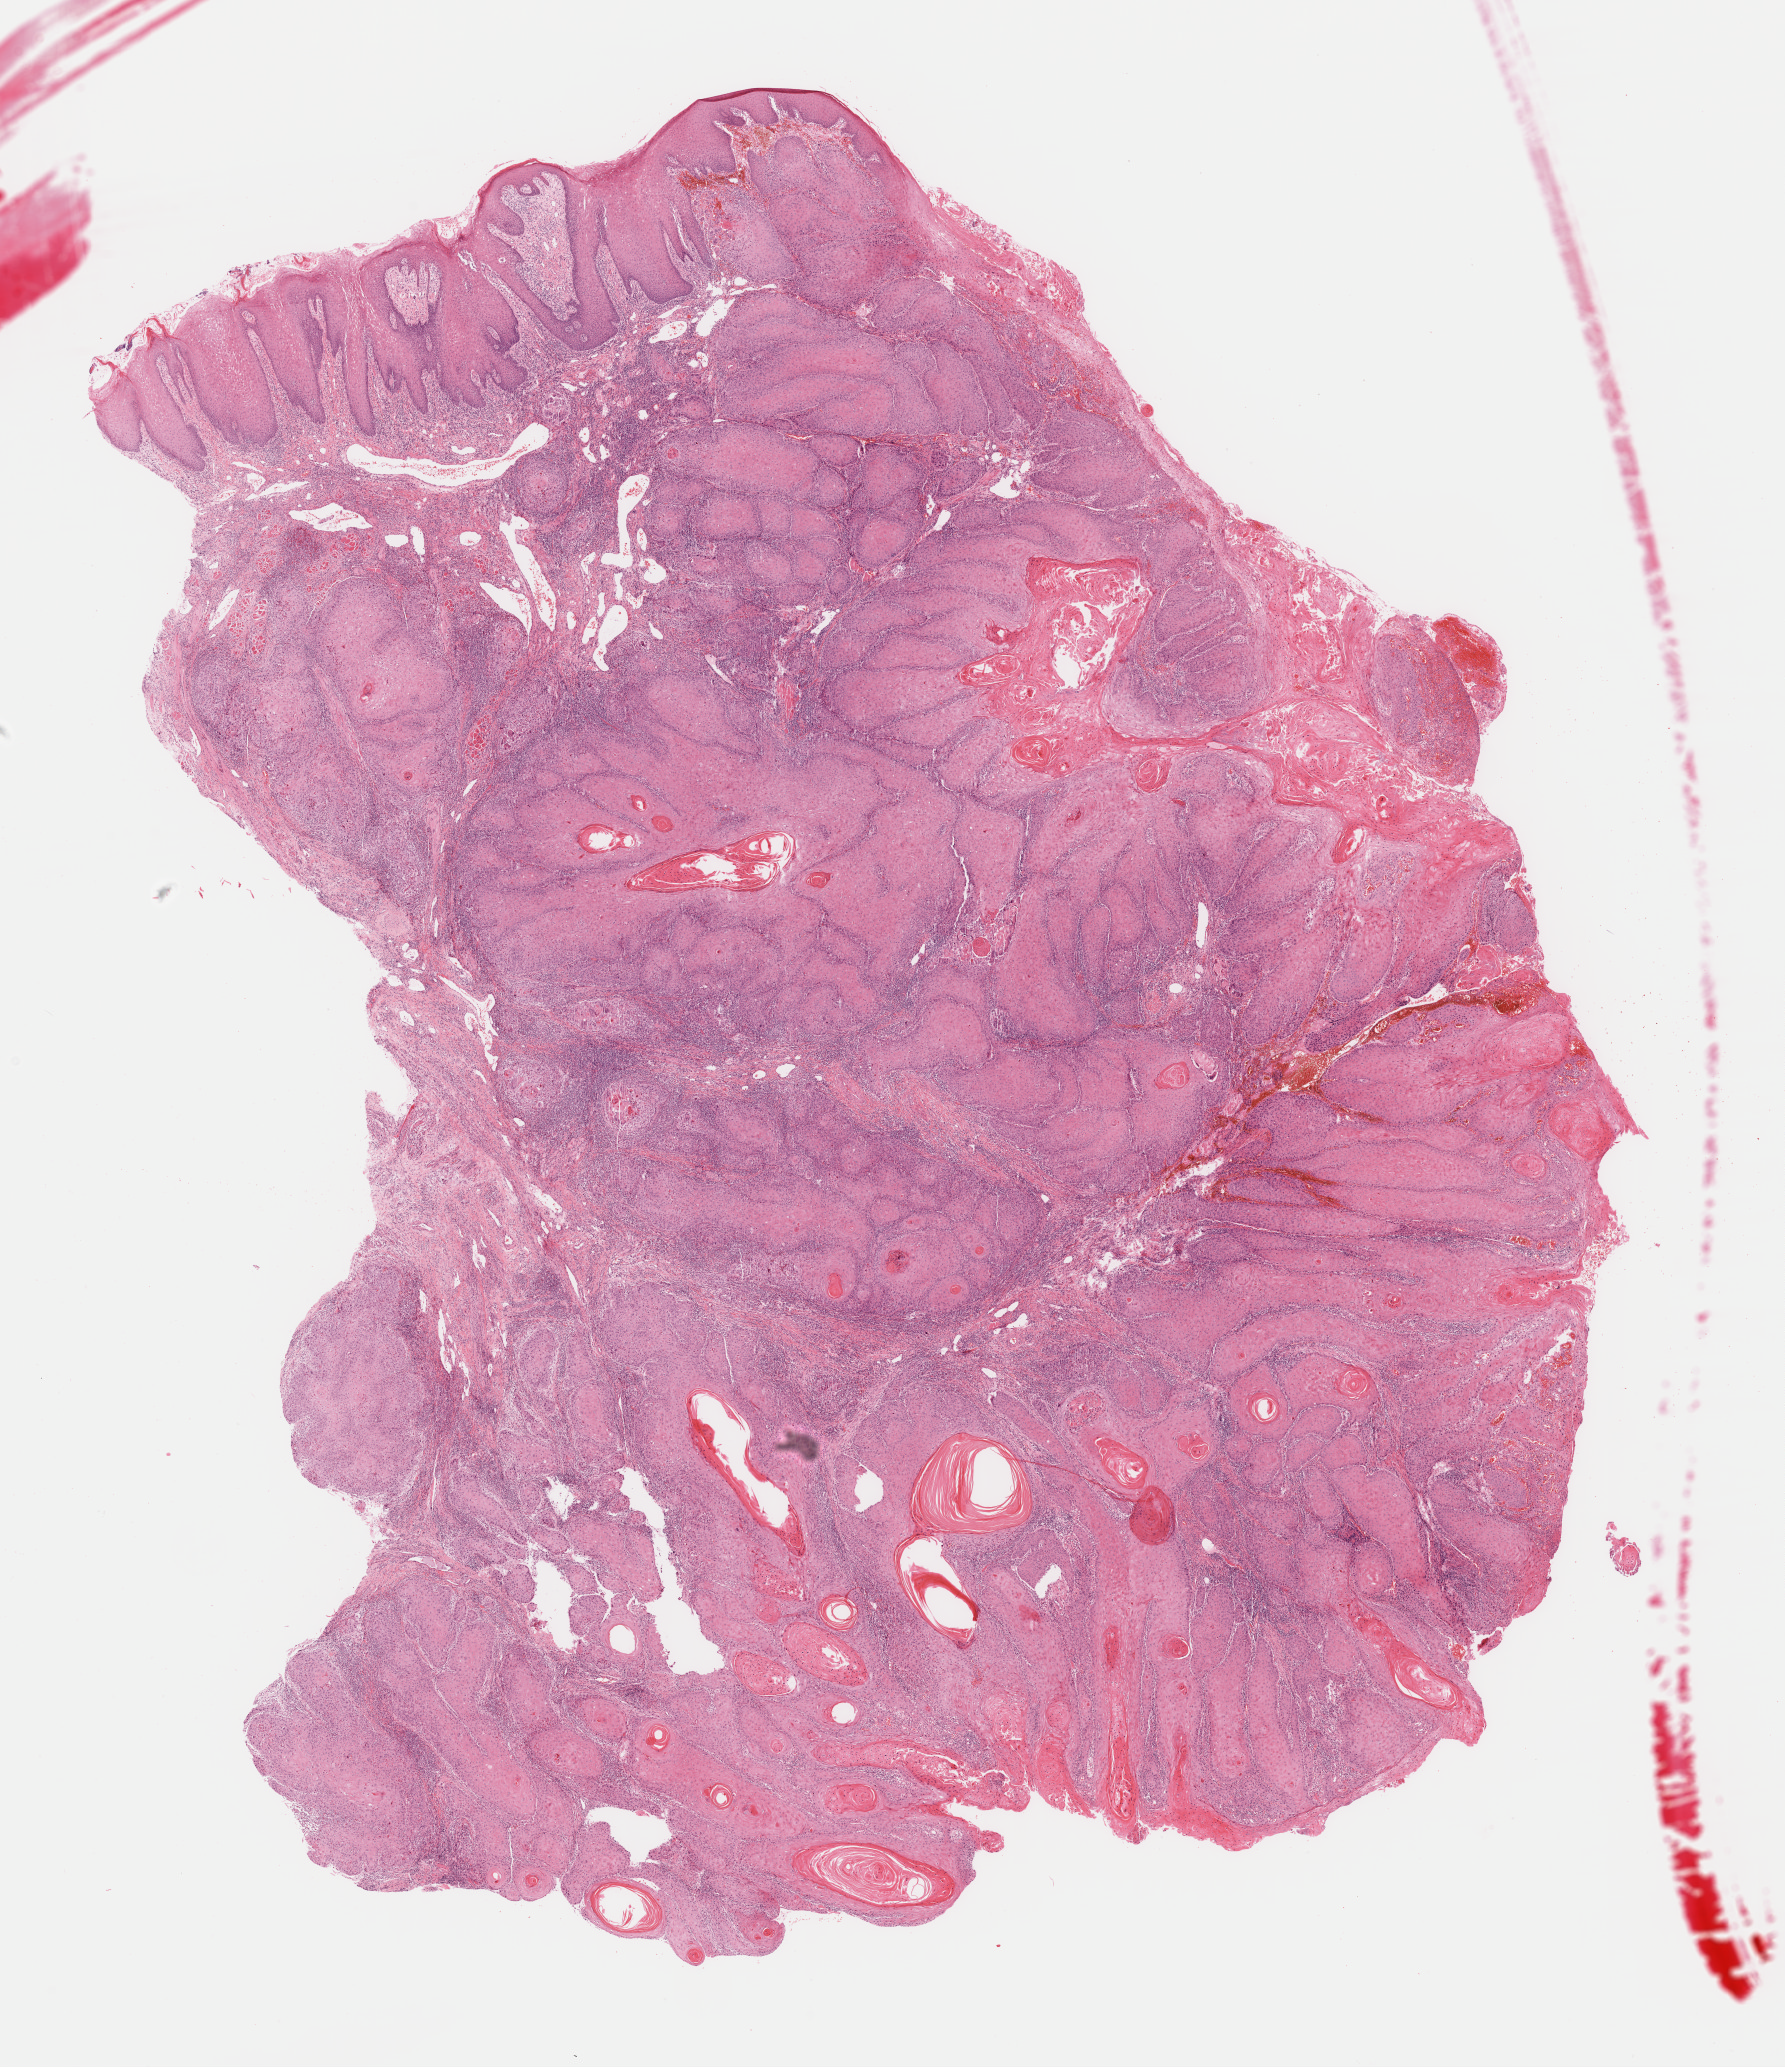
Hematoxylin and eosin (H&E) stained whole-slide image, whole scanned area (about 14.1 x 16.3 mm) shown as a low-resolution overview. Formalin-fixed paraffin-embedded (FFPE) diagnostic section. Primary tumour sample from the head and neck. Male, age 66 years at initial diagnosis. Histologic grade: G1 (well differentiated).
• AJCC pathologic stage: III (7th edition)
• TNM: T3 N1 M0
• pathologic diagnosis: Squamous cell carcinoma, NOS (tongue, NOS)